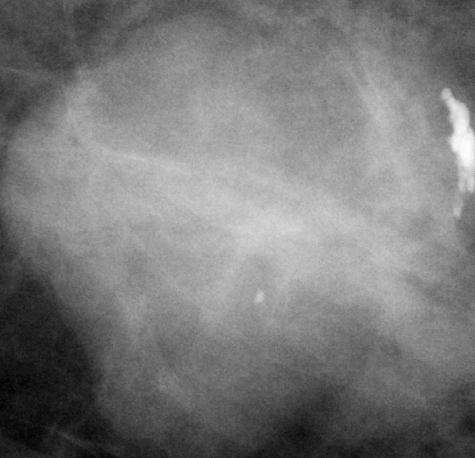
Crop from a digitized film mammogram around one marked abnormality, right breast, CC view.
Finding: mass, shape lobulated, margins circumscribed; BI-RADS assessment category 3; subtlety rating 5 on a 1 (subtle) to 5 (obvious) scale; pathology result (as recorded, not read from the image): benign.